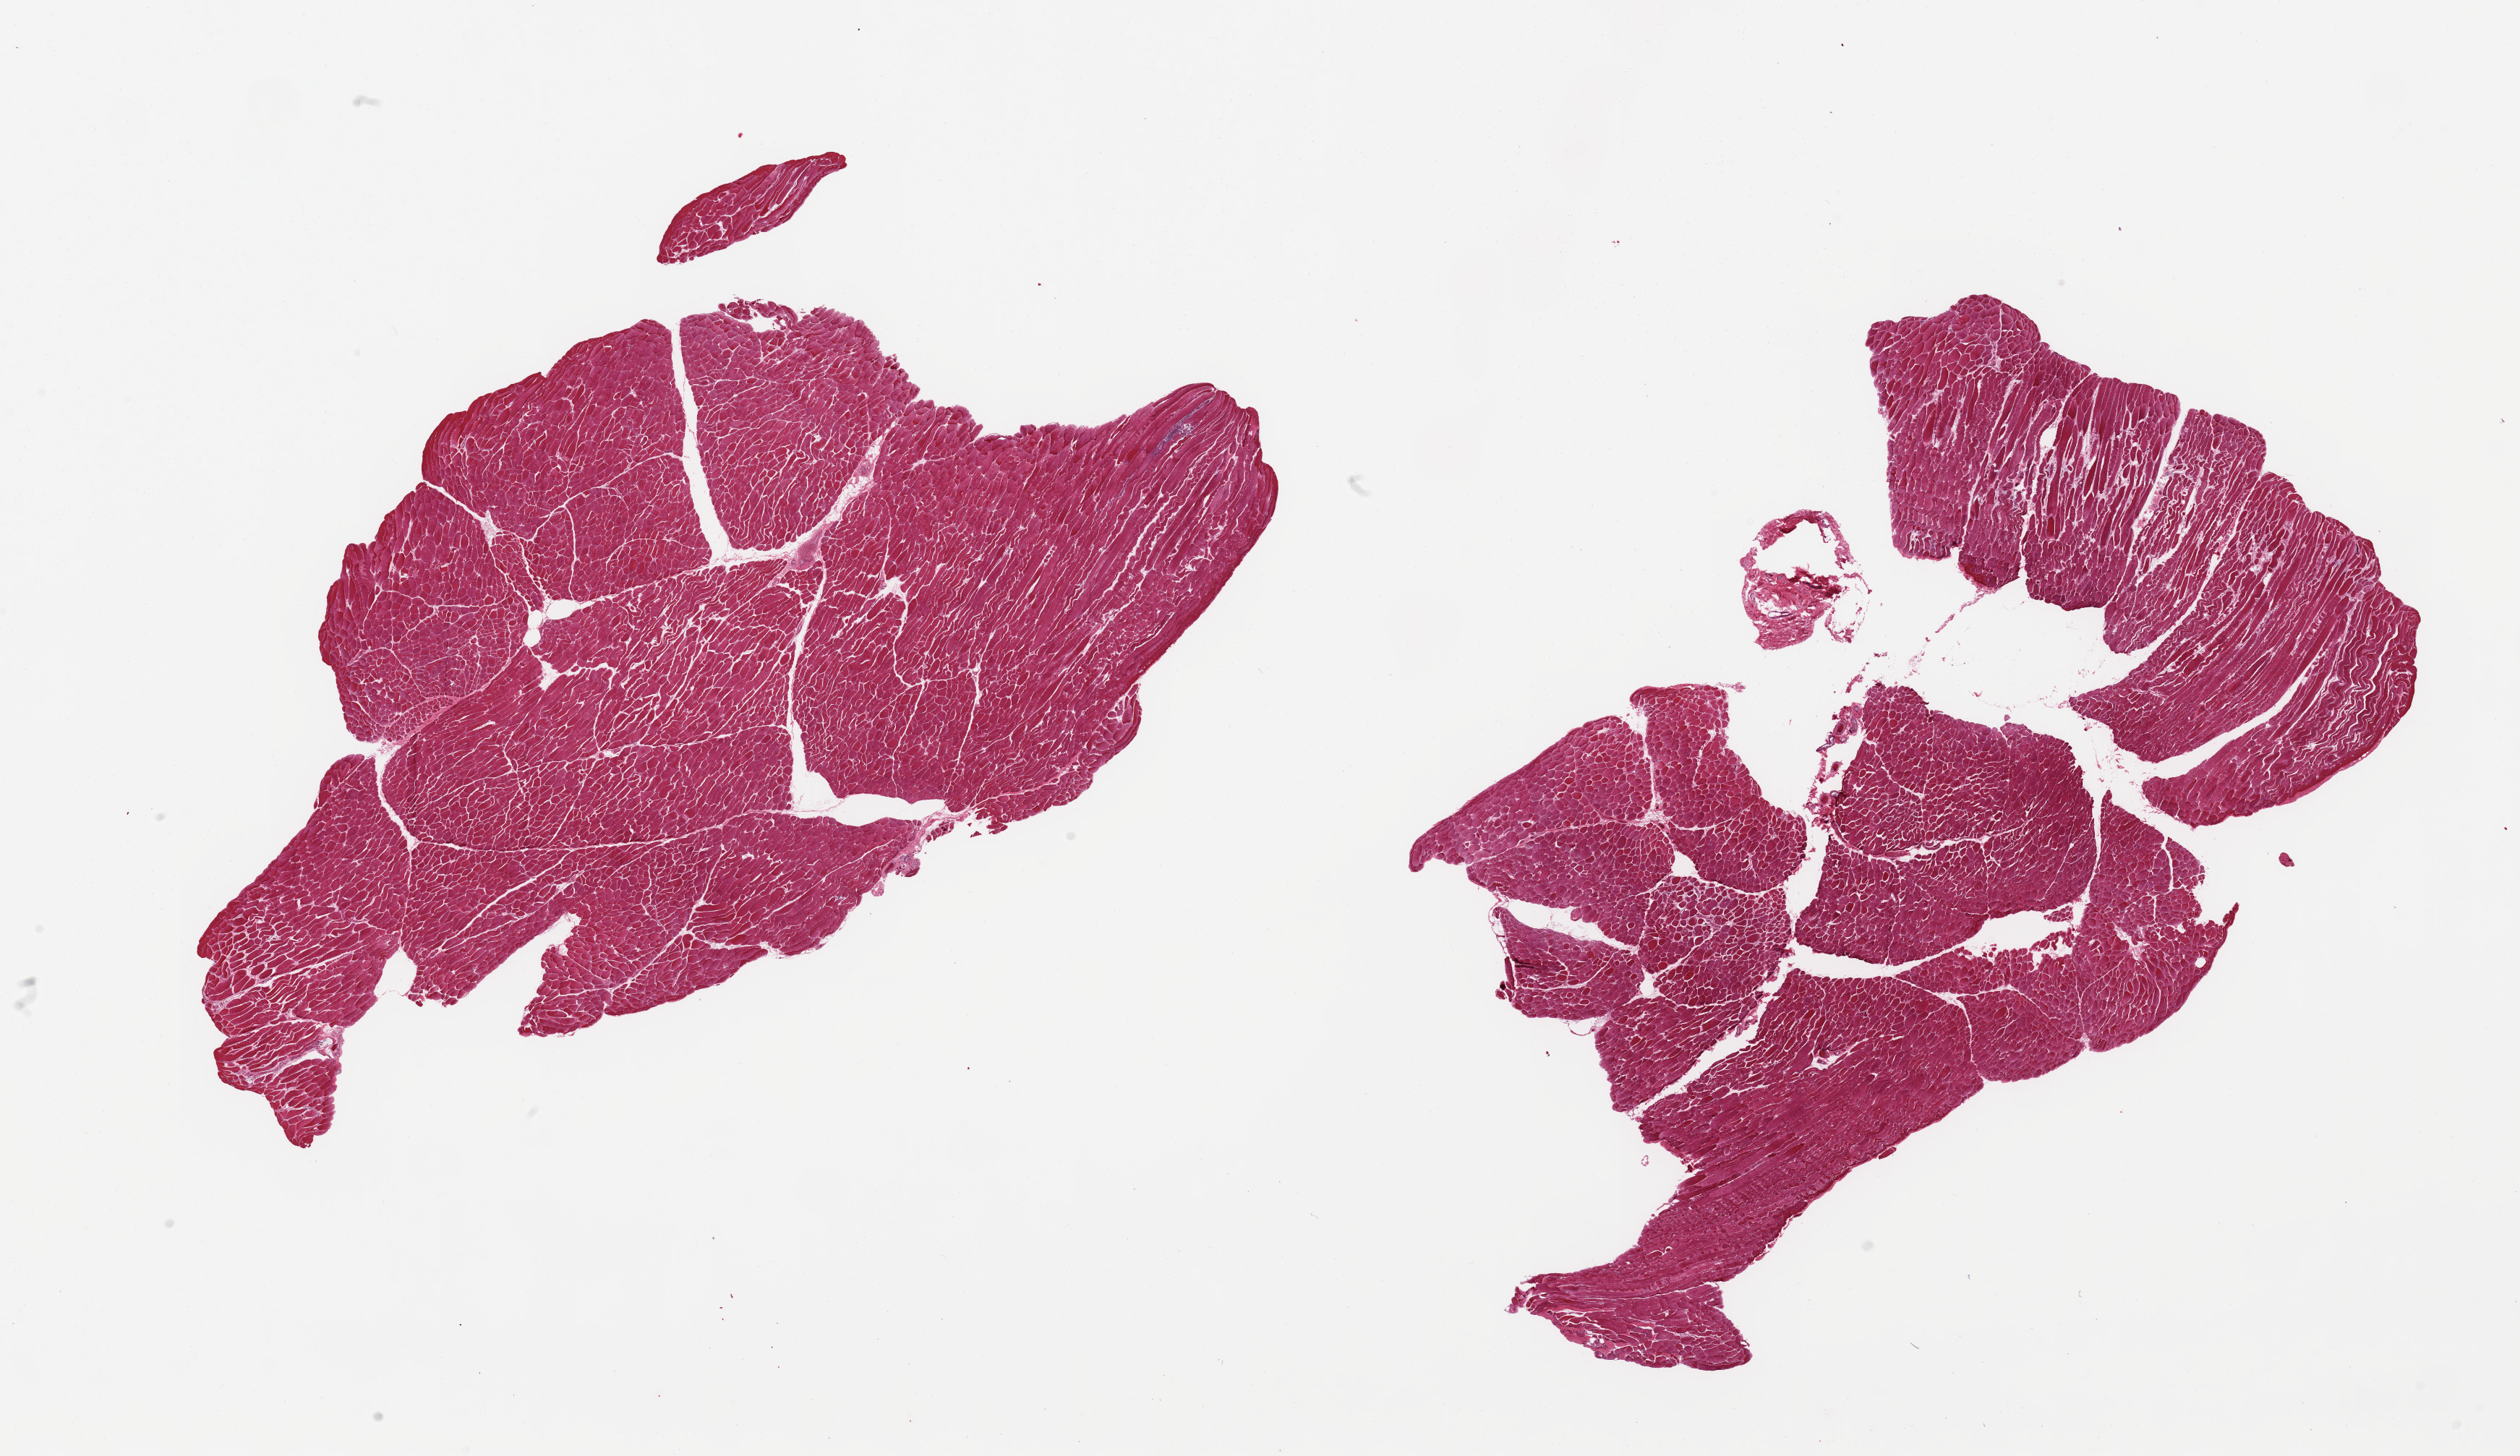
Digitized hematoxylin and eosin (H&E)-stained section, a low-resolution overview of the entire scanned area, about 27.6 x 15.9 mm (acquisition: 20x scan). PAXgene-fixed, paraffin-embedded tissue. Sampled site (target tissue): skeletal muscle. Donor tissue sample. Male donor.
Review note (as recorded): 2 pieces; <2% fat.